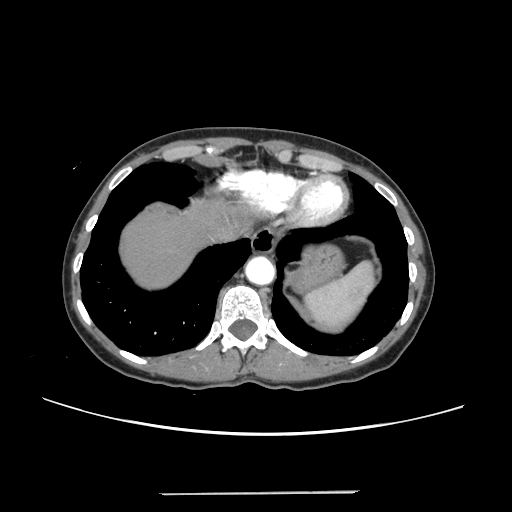
Contrast-enhanced abdominal CT, one axial slice. Position 218 of 240 along the scan axis. Intravenous contrast given. Soft-tissue window (W 400 / L 40 HU). 1.25 mm slice thickness. 512 × 512 image matrix, field of view 371 × 371 mm. Female patient, age 60 years. Case-level facts recorded for this patient, not image findings: diagnosis: colorectal cancer liver metastases, imaged before liver resection; multiple liver metastases: no; largest metastasis: 1.5 cm.
Outlined on this slice (expert manual segmentation):
- liver: bounding box [x1, y1, x2, y2] px = [122, 201, 231, 288]
- planned liver remnant (the part of the liver to remain after resection): [122, 201, 230, 288]